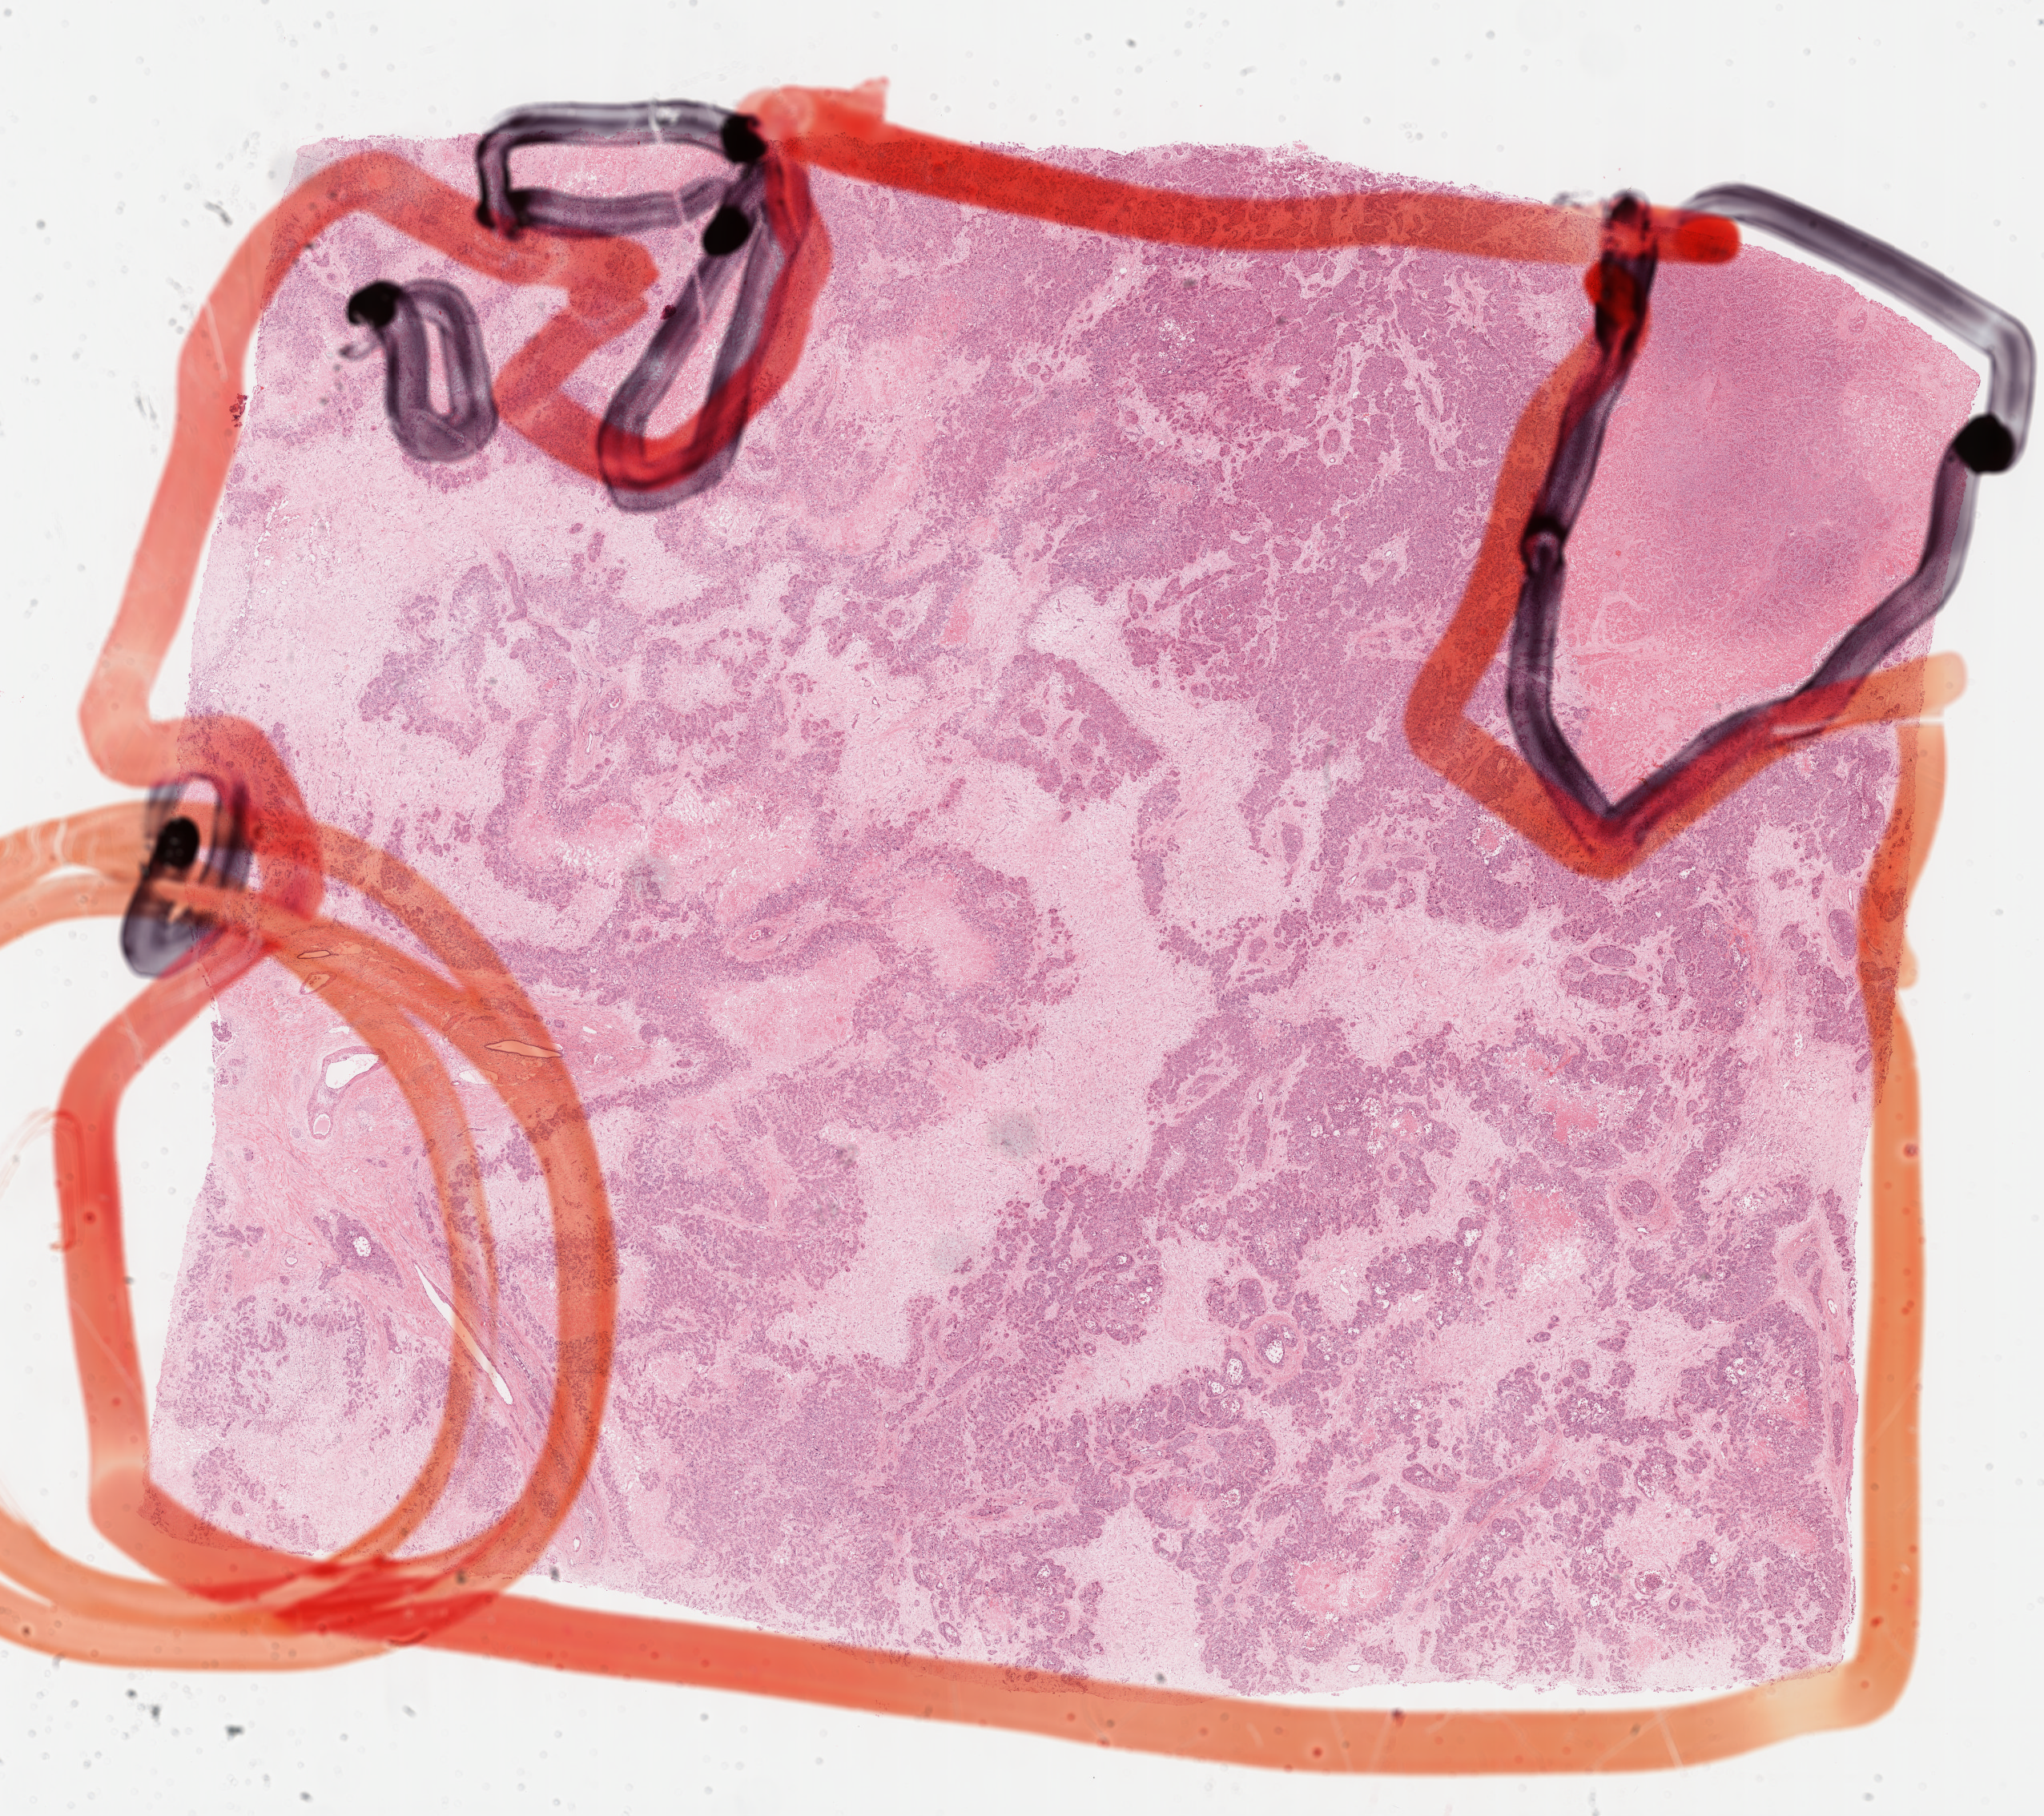
Whole-slide histology image, H&E-stained, shown as a low-resolution overview of the whole scanned area (about 20.6 x 18.3 mm). FFPE section. Liver, primary tumour sample. Female patient; age at initial diagnosis 48 years. Histologic grade: G3 (poorly differentiated).
- histologic diagnosis: Hepatocellular carcinoma, NOS
- AJCC pathologic stage: II (7th edition)